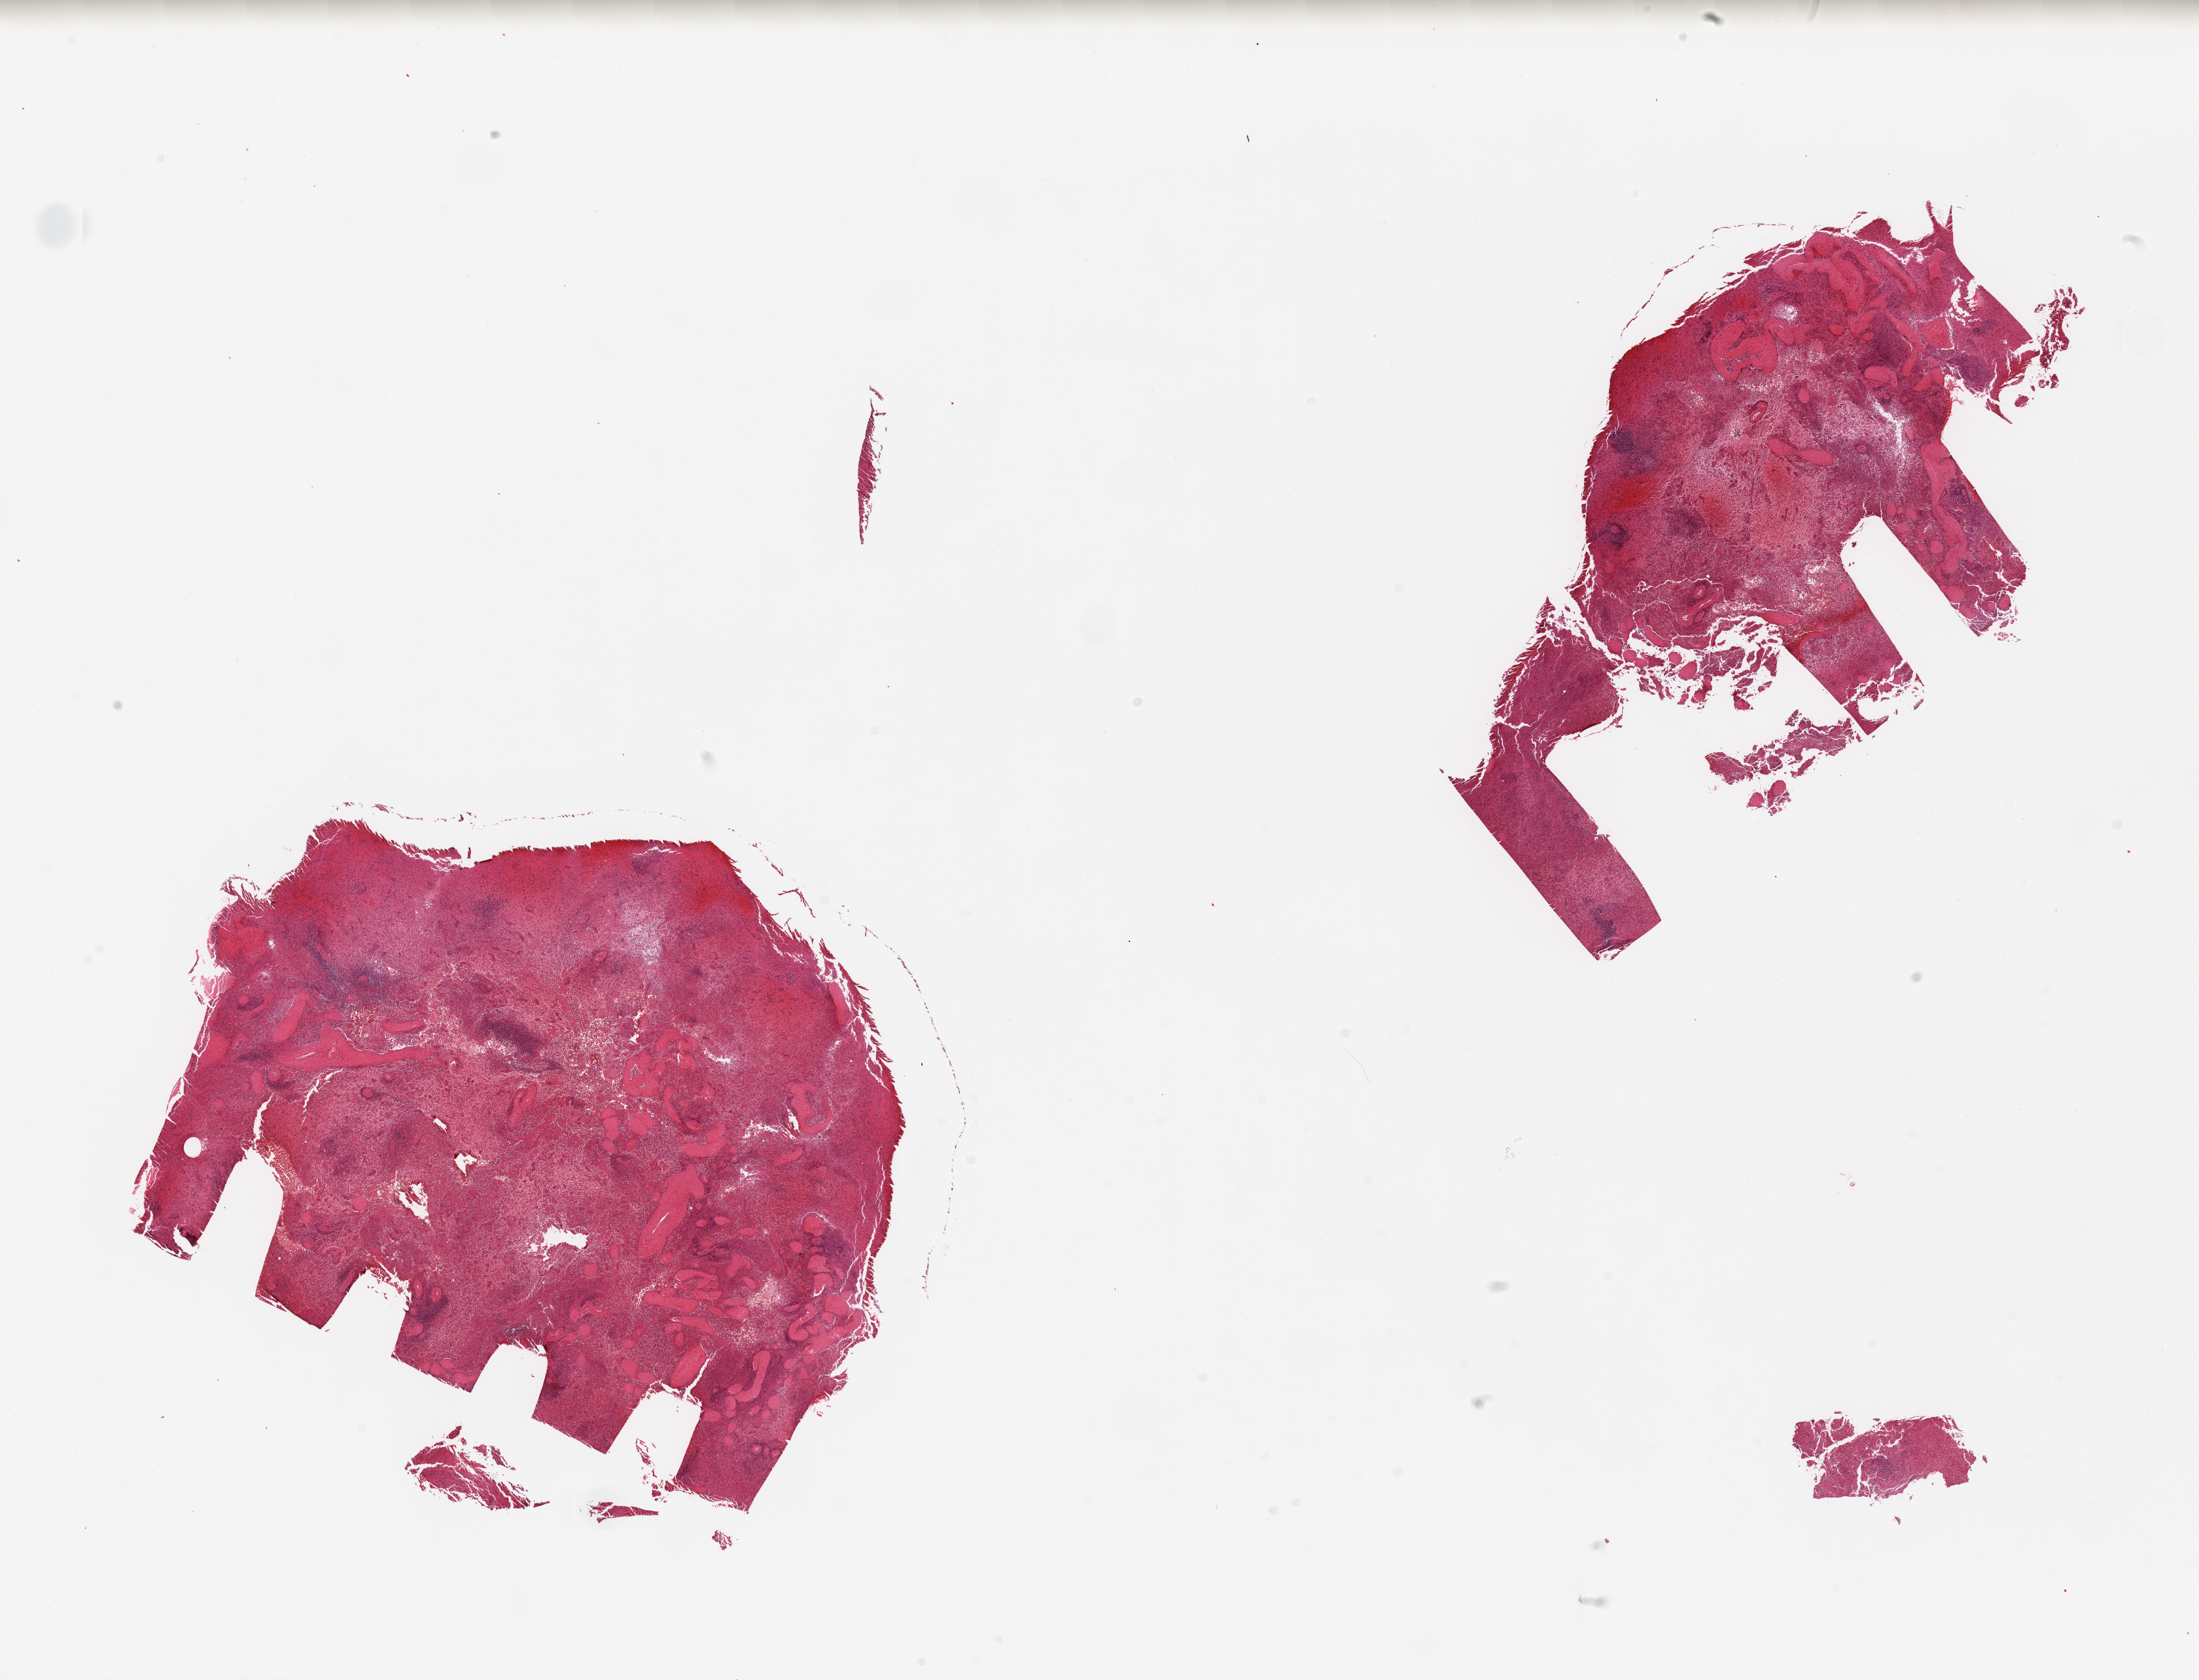
Digitized H&E-stained section, low-resolution overview of the scanned area, about 26.6 x 20.3 mm (slide scanned at 20x), PAXgene-fixed, paraffin-embedded tissue, sampled site (target tissue): spleen, tissue donor sample. Donor: male.
Reviewer comment on this tissue sample: 2 pieces; marked congestion.